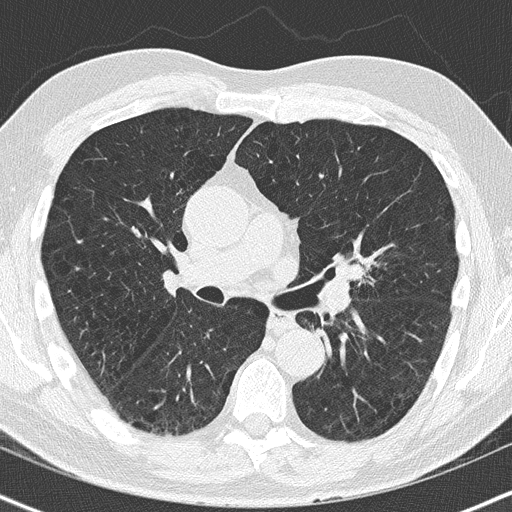
Low-dose screening chest CT, axial slice. Baseline screening round. Lung window (W 1500 / L -600 HU). Lung (sharp) reconstruction kernel (B50f). Slice 73 of 163 in the series. 512 × 512 image matrix. Male participant, aged 63 years at enrolment. Former smoker at enrolment.
Expert-annotated lung lesion, bounding box (x1, y1, x2, y2) in pixels: (330, 251, 375, 289). The screening reader recorded 2 non-calcified nodules or masses ≥4 mm on this exam (lingula, right lower lobe); which of them this box marks is not recorded. Lung cancer was diagnosed 32 days after this screen: squamous cell carcinoma, NOS, left upper lobe, moderately differentiated (G2), stage IA (AJCC 6th edition), 23 mm at pathology.